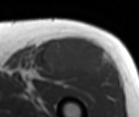
MRI of an extremity soft-tissue mass, one axial slice. Slice 69 of 86 in the series (ordered by position). MR volume resampled by the dataset authors to the PET/CT grid (not the native acquisition matrix). 3.27 mm slice thickness. 139 × 117 image matrix, field of view 136 × 114 mm. Male patient. Case-level facts recorded for this patient, not image findings: histological type: extraskeletal osteosarcoma; grade: high; site of the primary tumour: thigh.
Outlined on this slice (expert contour drawn on MRI and transferred to this co-registered scan by the dataset authors):
- gross tumour volume (mass): bounding box <42,41,107,78> (left, top, right, bottom; pixels)